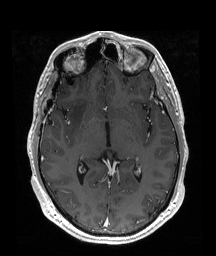
Brain MRI from a brain-tumour surgery series, one axial slice. Slice 107 of 192 in the series (ordered by position). T1-weighted post-contrast. 1 mm slice thickness. 216 × 256 image matrix, field of view 219 × 260 mm. Case-level facts recorded for this patient, not image findings: histopathology: Astrocytoma; WHO grade: 2; IDH mutation: yes.
Structures marked on this image (outlined manually by an expert reader):
- tumour: bounding box <71,94,91,132> (left, top, right, bottom; pixels)